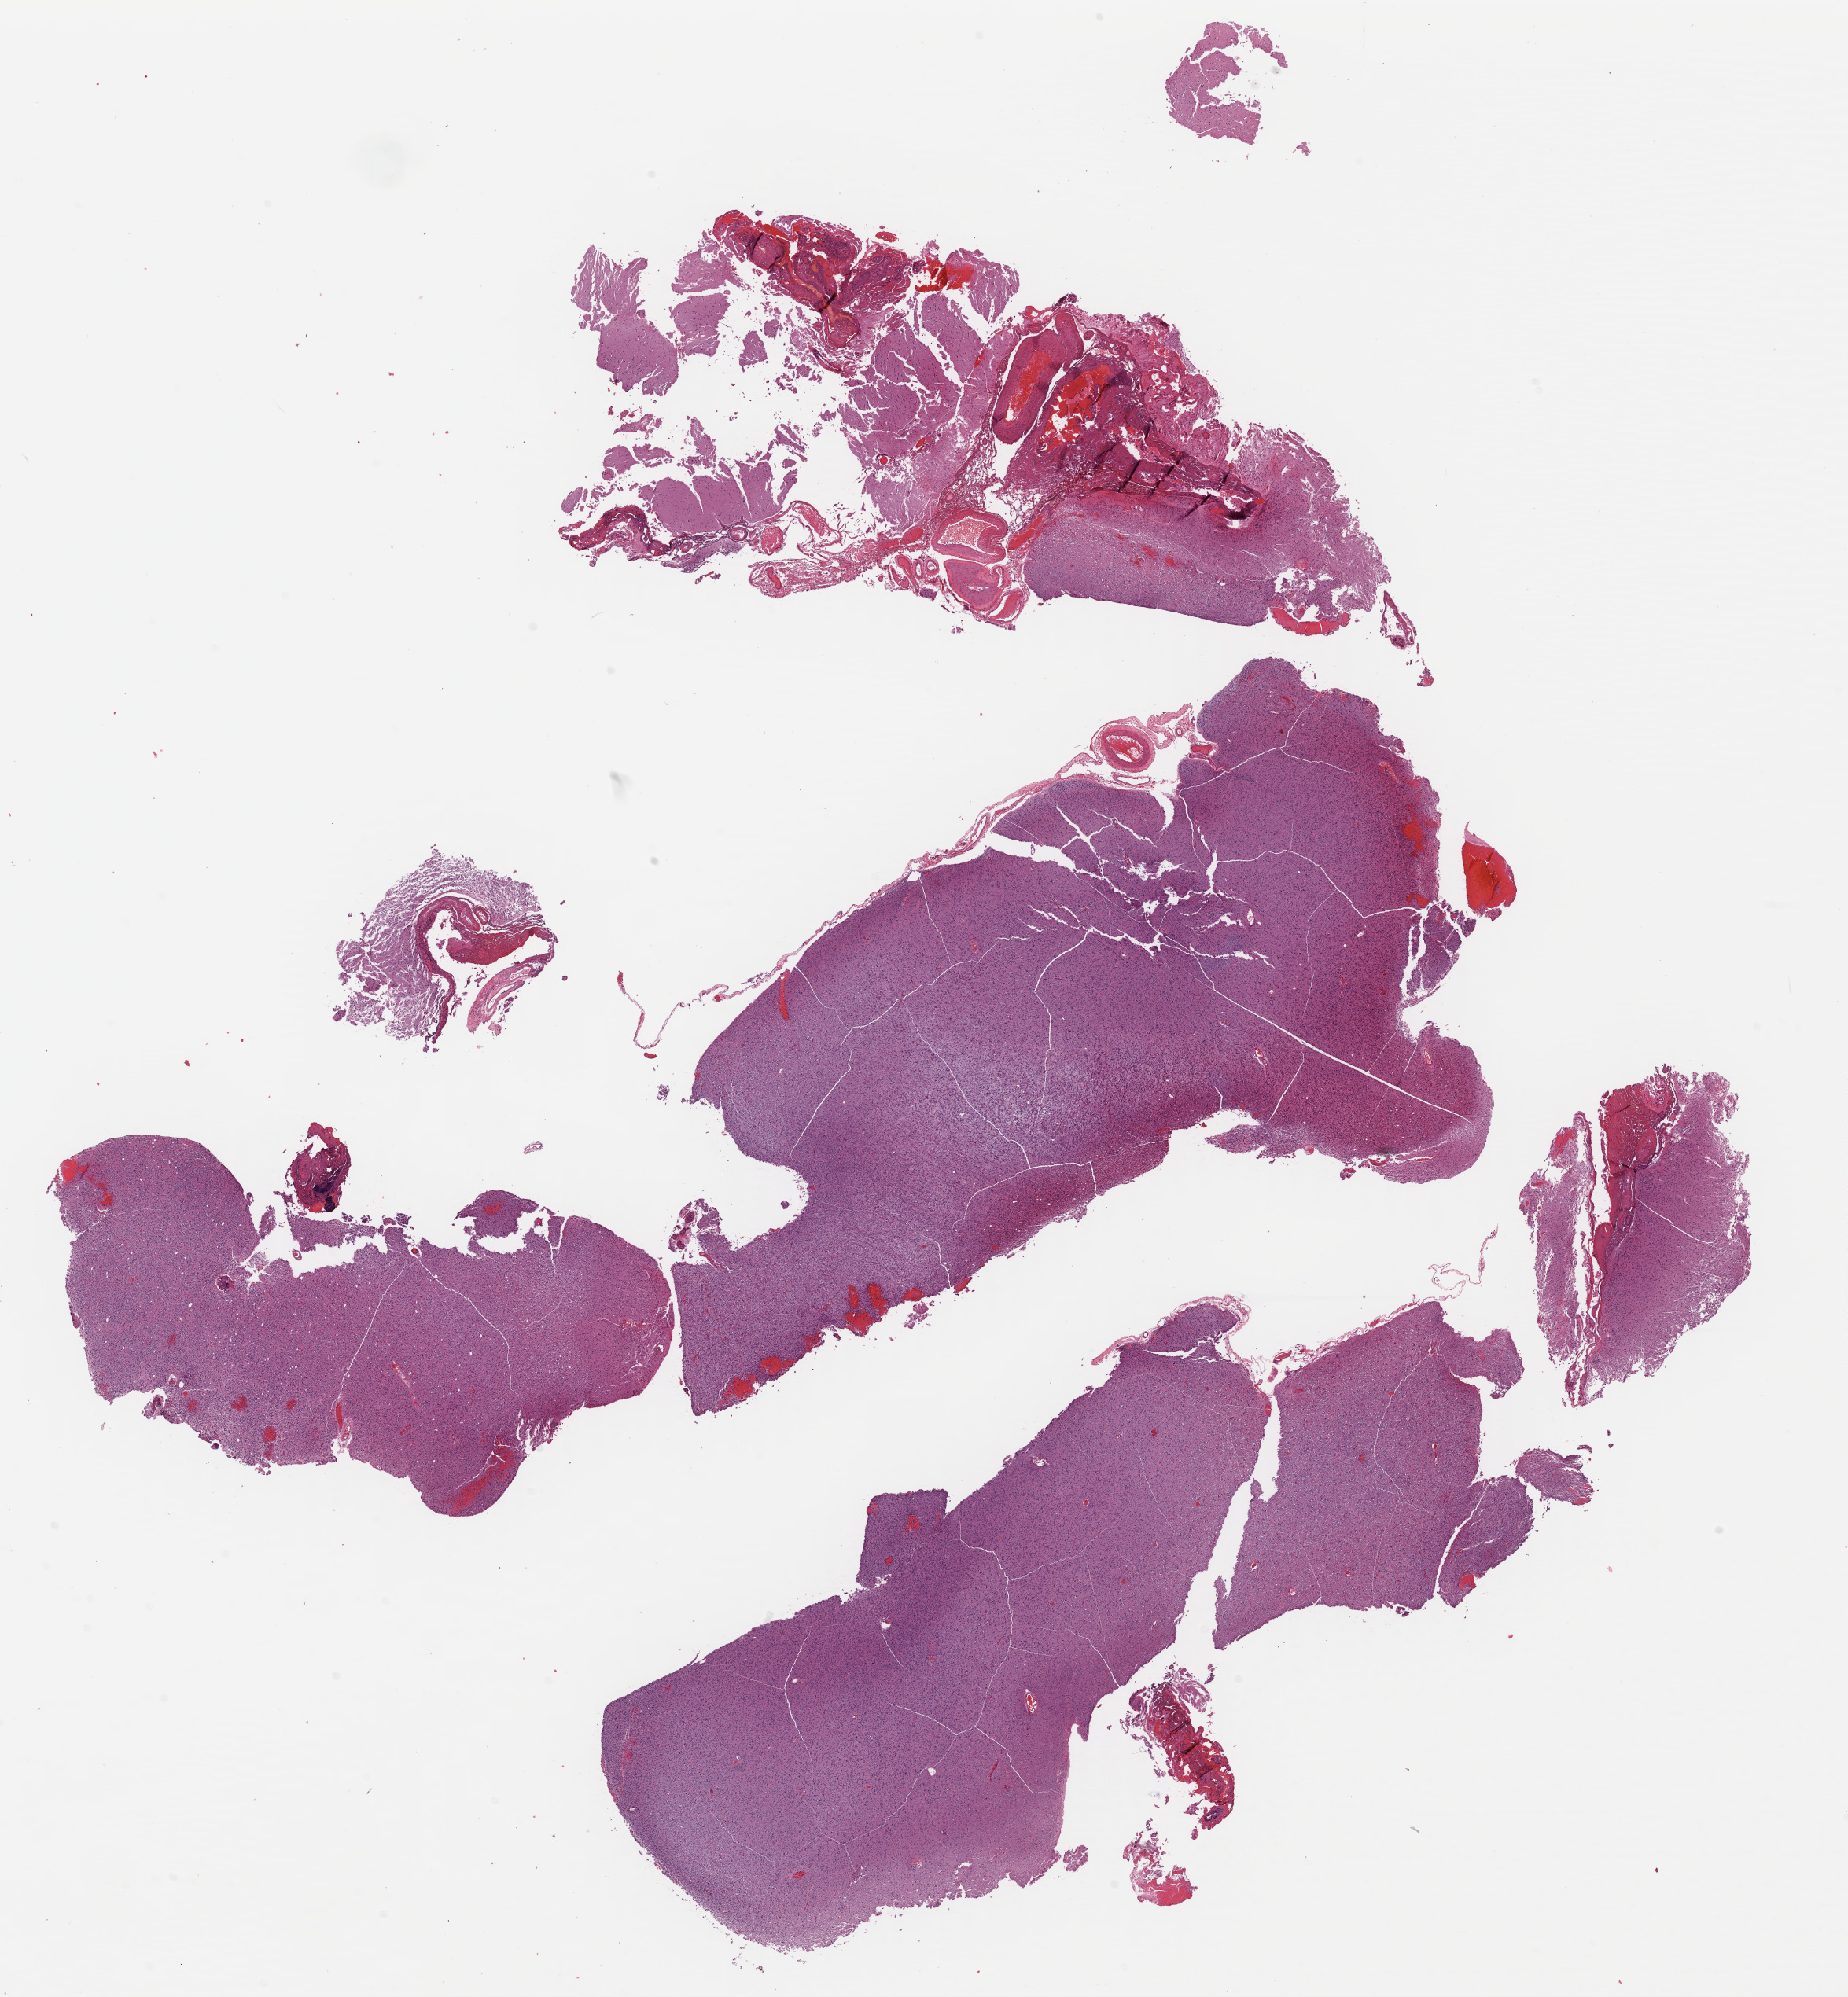
H&E-stained whole-slide image, low-resolution overview of the scanned area, about 18.5 x 20.0 mm (slide scanned at 40x); formalin-fixed paraffin-embedded (FFPE) diagnostic section; primary tumour sample from the brain. Male patient; age at initial diagnosis 56 years. Histologic grade: G2 (moderately differentiated).
Histologic diagnosis: Oligodendroglioma, NOS (cerebrum). Laterality: left.